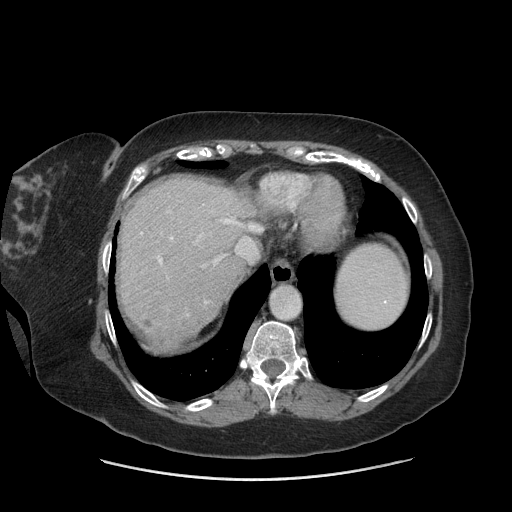
Contrast-enhanced abdominal CT (liver protocol), one axial slice; slice 60 of 69 in the series (ordered by position); reconstruction kernel STANDARD; 140 kVp; soft-tissue window (W 400 / L 40 HU); 2.5 mm slice thickness; 512 × 512 image matrix, field of view 420 × 420 mm. Case-level facts recorded for this patient, not image findings: diagnosis: hepatocellular carcinoma (patient treated with transarterial chemoembolisation; whether this scan precedes or follows treatment is not stated here); TNM stage (as recorded): Stage-IIIB; Child-Pugh class: A; tumour nodularity: multinodular.
Structures marked on this image (semi-automatic segmentation, software-assisted and operator-edited):
- abdominal aorta: bounding box (x1, y1, x2, y2) in pixels: (270, 286, 300, 319)
- liver parenchyma outside the tumour (the mass and vessels are separate outlines, so this box may not span the whole liver): (118, 176, 256, 348)
- mass: (141, 295, 217, 347)
- liver vessels: (141, 218, 252, 264)